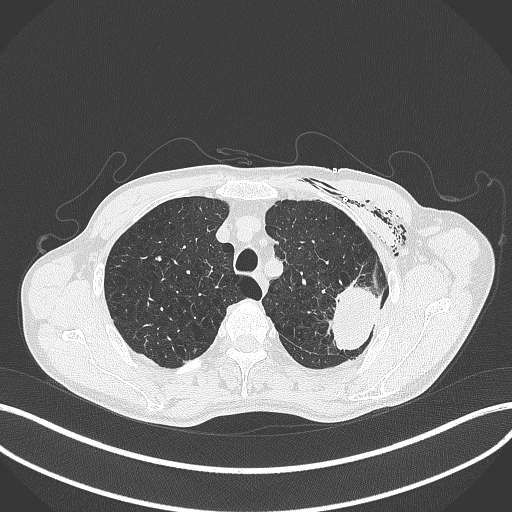
Chest CT, one axial slice. Position 329 of 457 along the scan axis. 120 kVp. Lung window (W 1500 / L -600 HU). 512 × 512 image matrix. Patient: male, 58 years. Case-level facts recorded for this patient, not image findings: clinical TNM (as recorded): T3 N0 M0.
Outlined on this slice (bounding box drawn by a radiologist):
- lung tumour (recorded histology: adenocarcinoma): bounding box <328,276,384,355> (left, top, right, bottom; pixels)